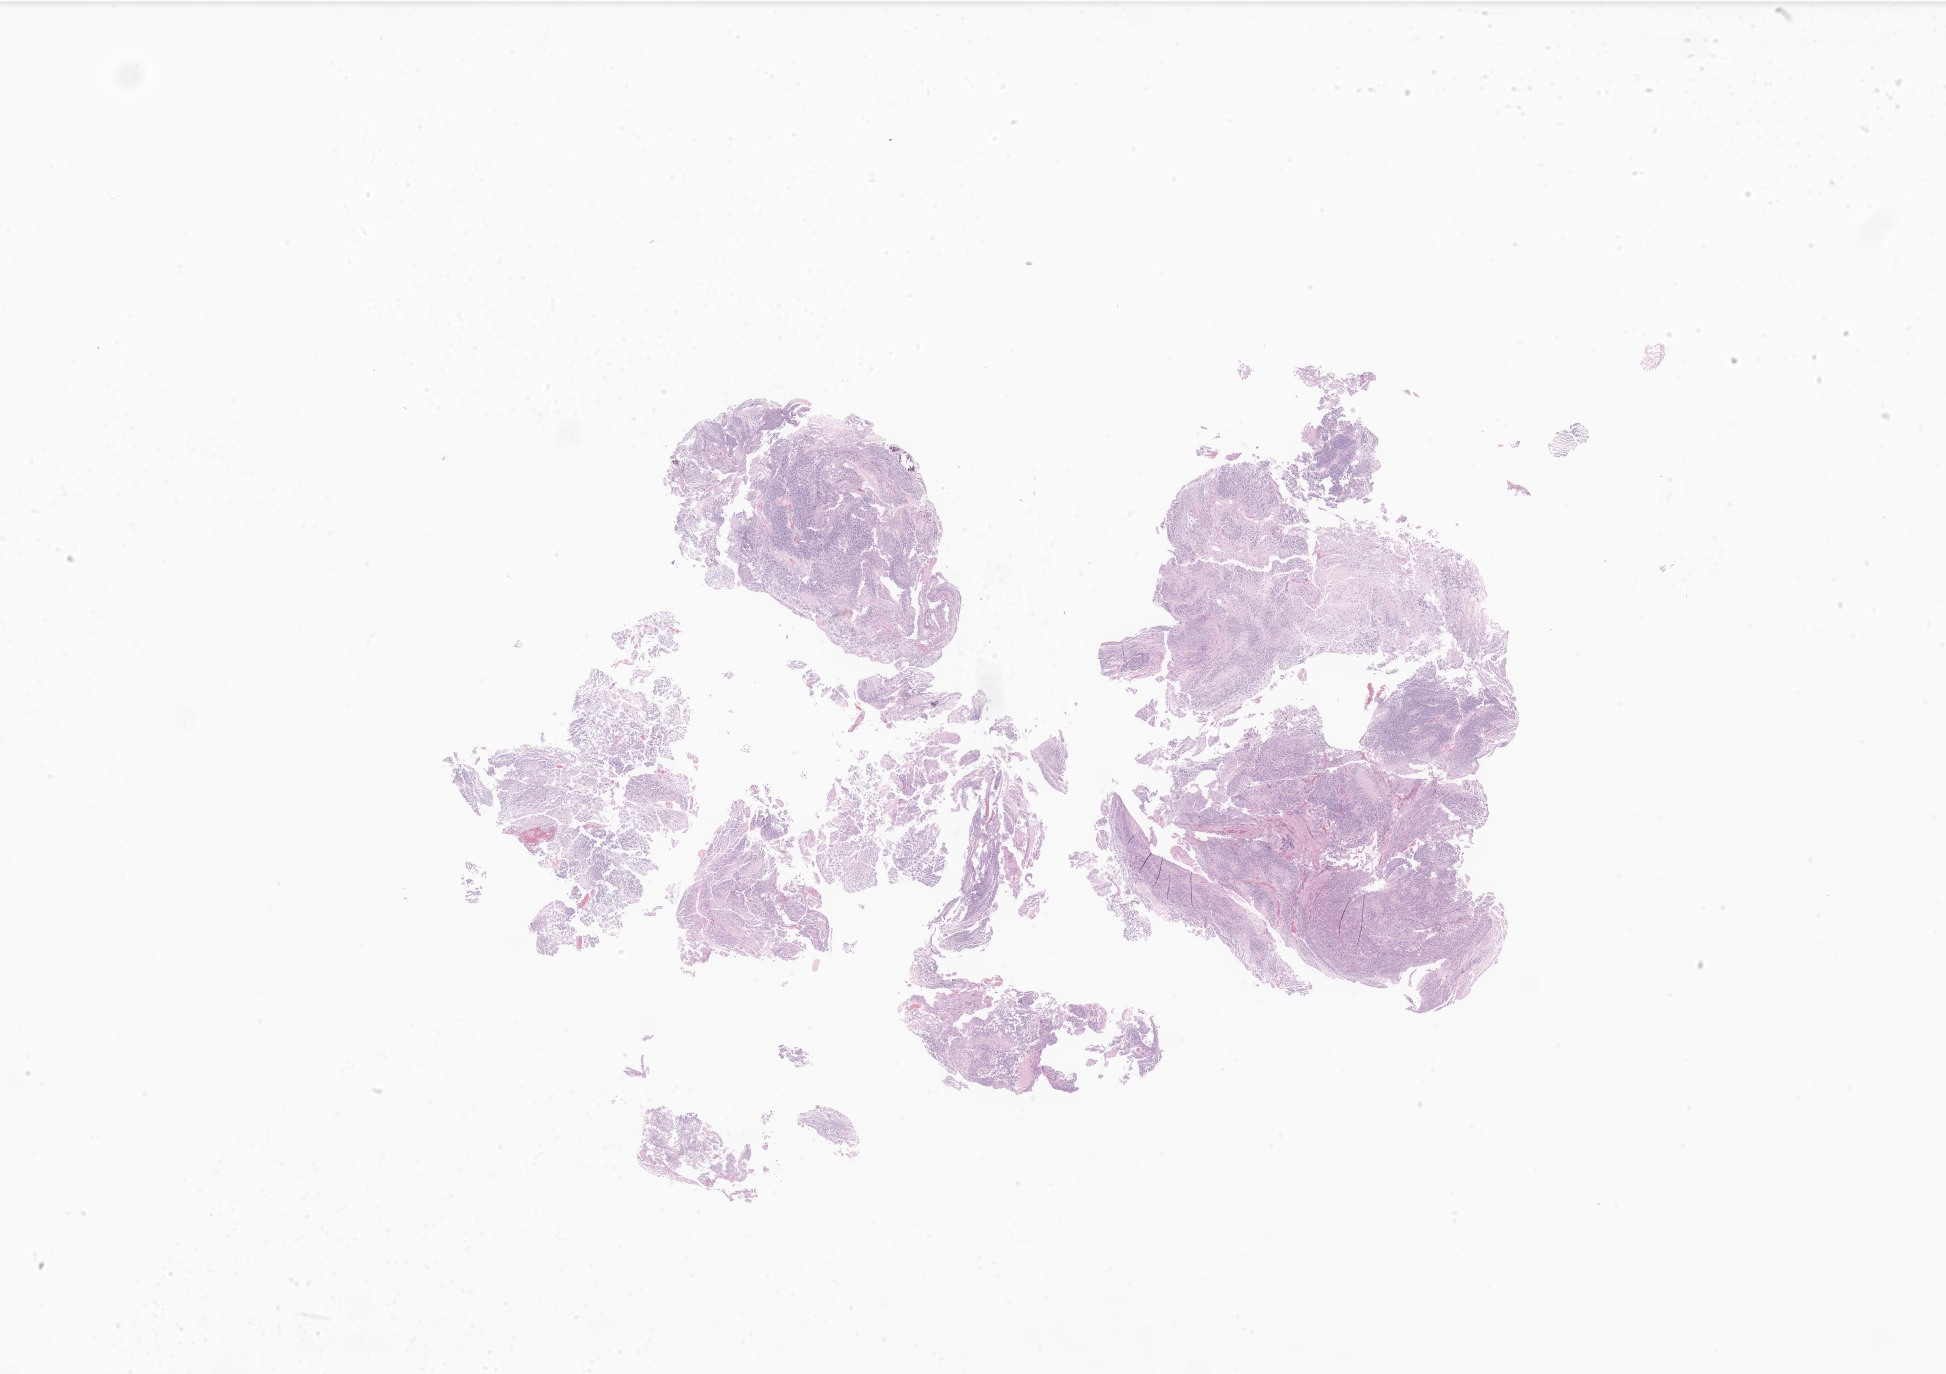
H&E whole-slide image of tumor tissue from the brain — low-resolution overview of the scanned area, about 32.8 x 23.2 mm, FFPE section. Patient female; age 218 months (18 years 2 months).
• diagnosis (ICD-O-3 morphology term): Neuroblastoma, NOS